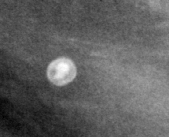
Cropped region of a digitized screen-film mammogram centred on a radiologist-marked abnormality, left breast, MLO view, BI-RADS breast density category 4 (scale 1–4).
- Finding: calcifications, morphology round and regular / lucent center / punctate, distribution diffusely scattered; BI-RADS assessment category 2; subtlety rating 5 on a 1 (subtle) to 5 (obvious) scale; benign; no additional work-up was recommended (benign without callback).